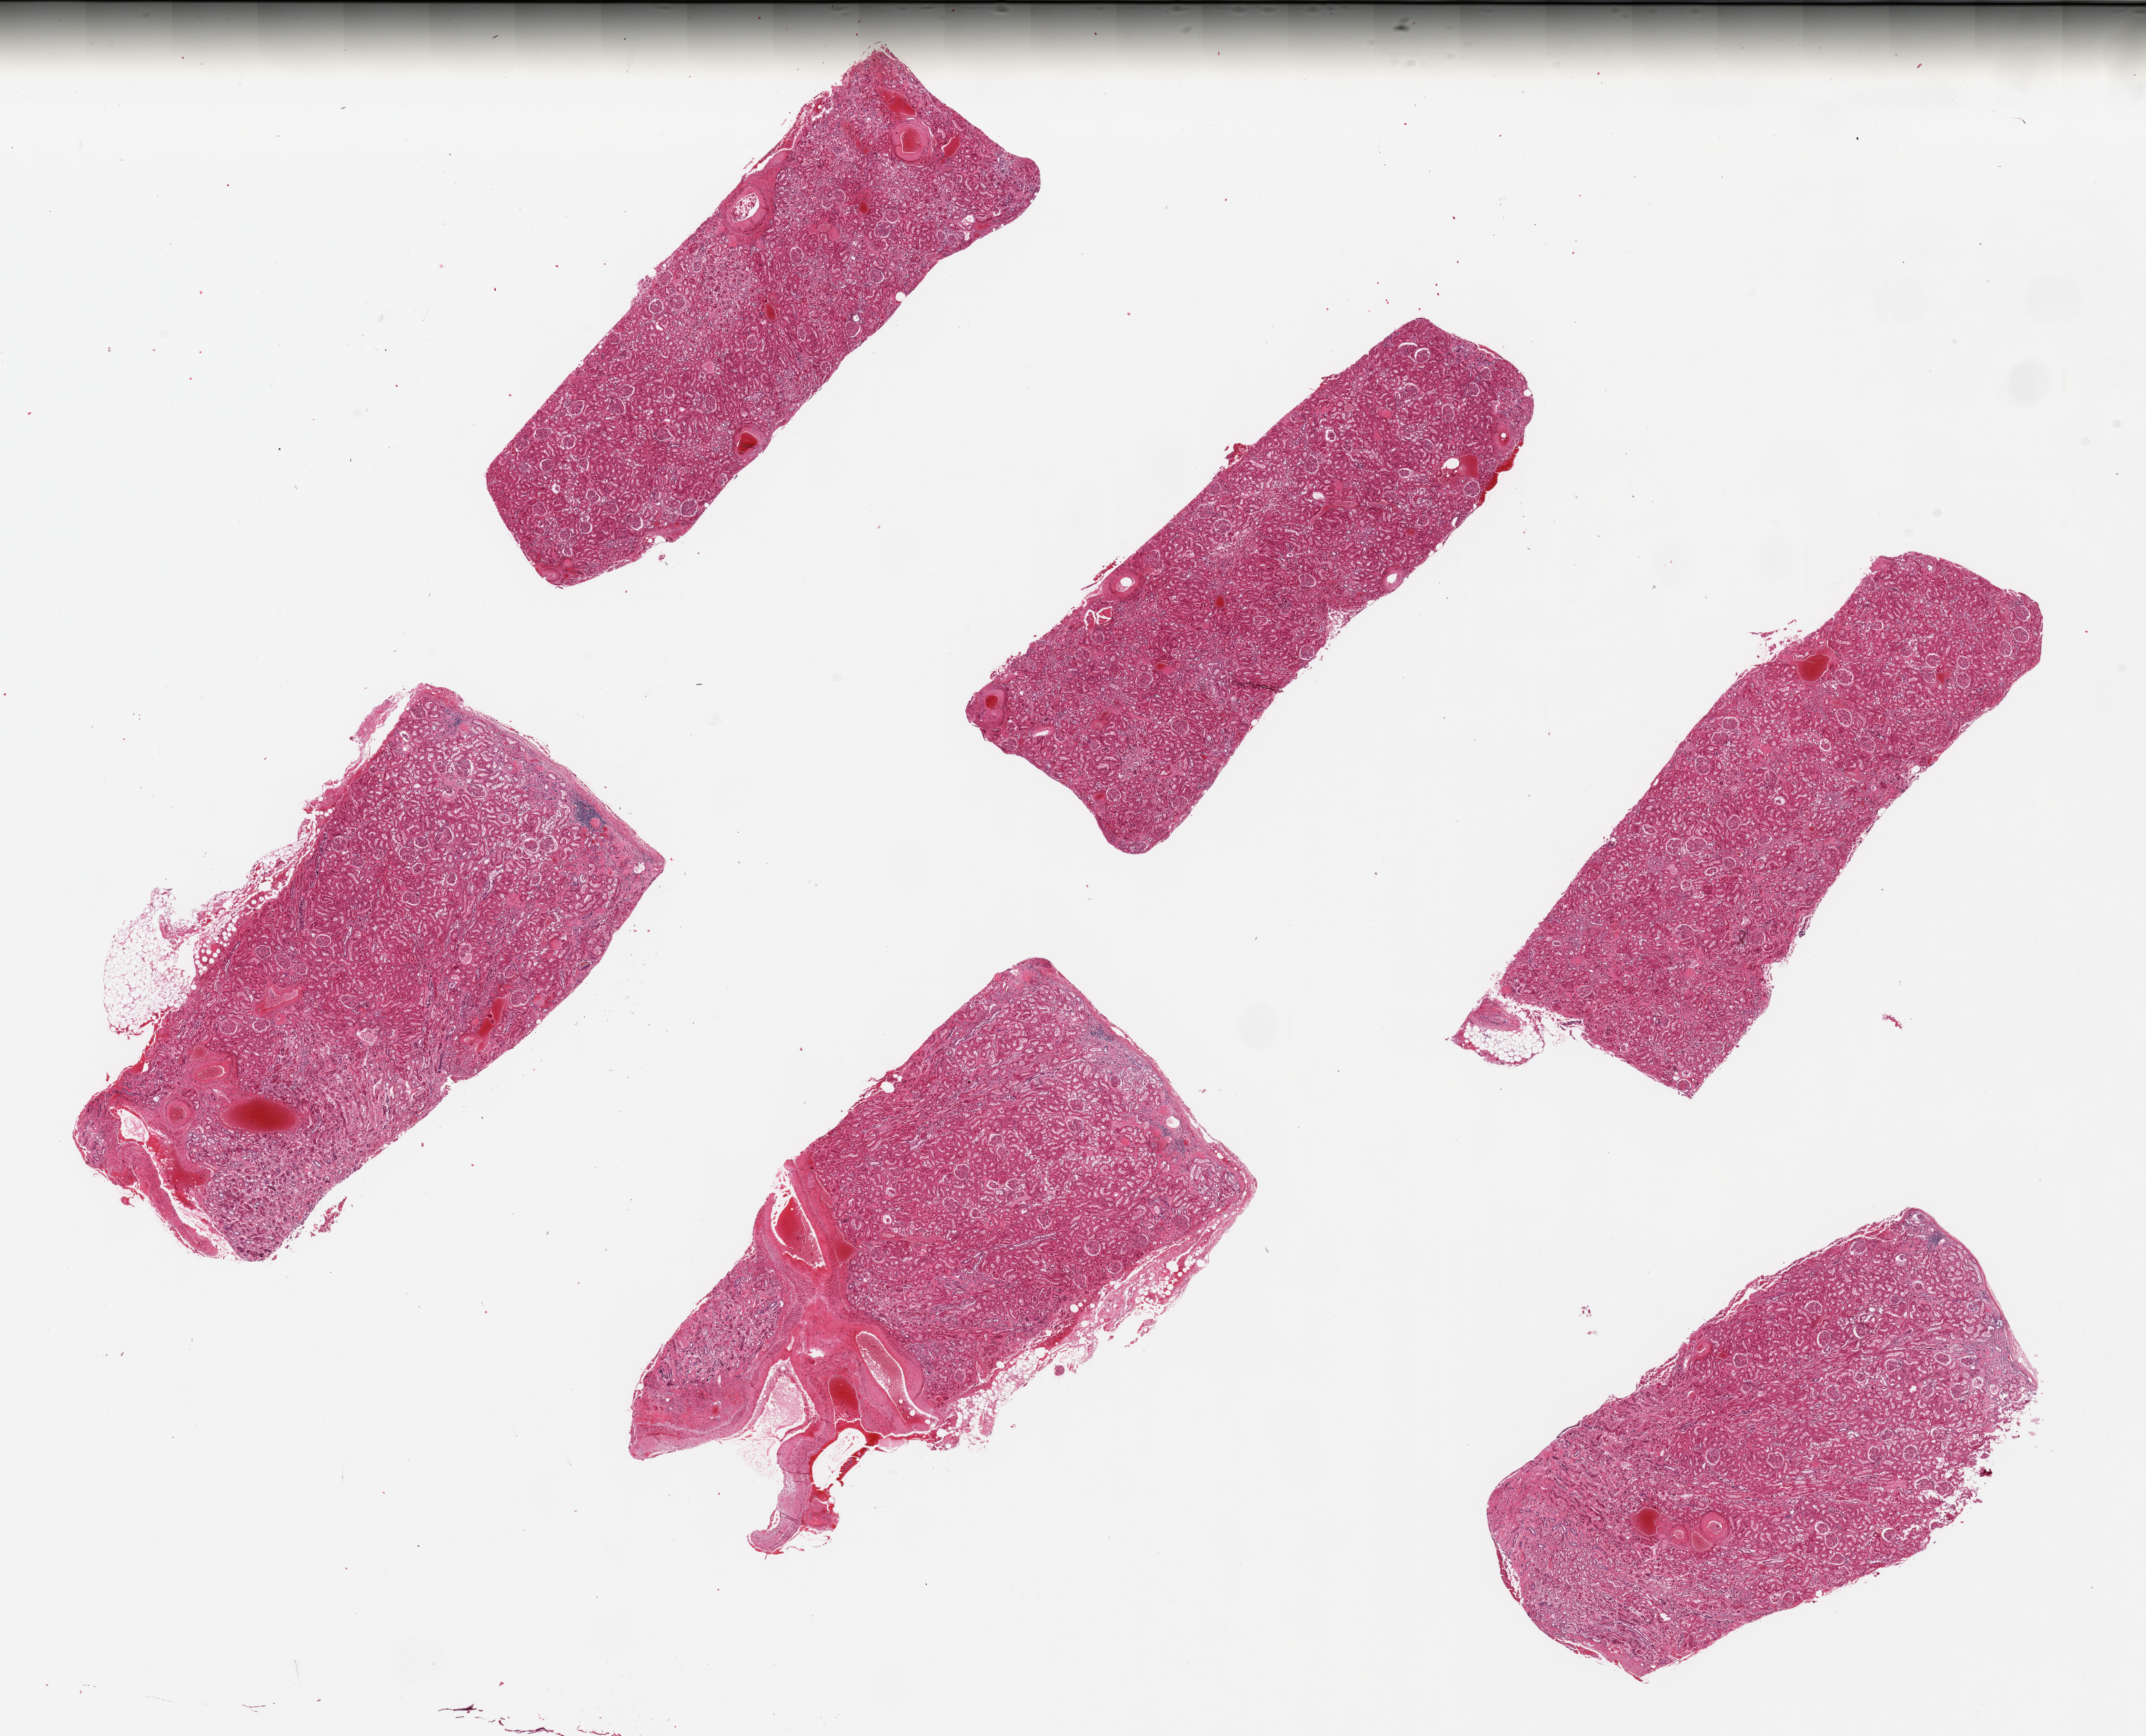
Whole-slide image, H&E stain, whole scanned area (about 24.6 x 19.9 mm, acquisition: 20x scan) shown as a low-resolution overview. PAXgene-fixed paraffin-embedded (PFPE) section. Section of renal cortex (target tissue). Tissue donor sample.
Review note (as recorded): 6 pieces, up to 8x3mm; arterionephrosclerosis with focal fibrosis.